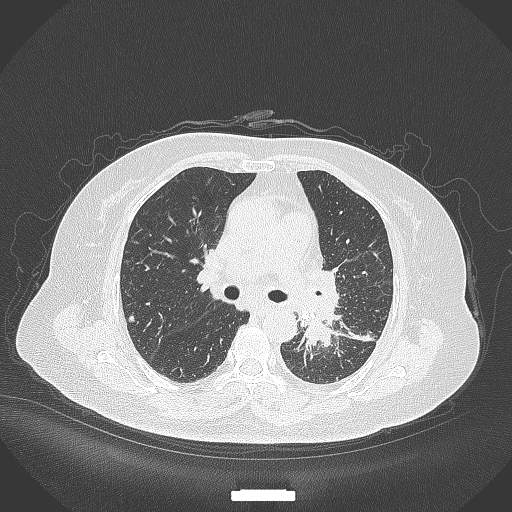
Chest CT, one axial slice; slice 210 of 322 in the series (ordered by position); lung window (W 1500 / L -600 HU); 1 mm slice thickness; 512 × 512 image matrix. Female patient, age 69 years. Case-level facts recorded for this patient, not image findings: clinical TNM (as recorded): T2b N3 M1.
Outlined on this slice (bounding box drawn by a radiologist):
- lung tumour (recorded histology: adenocarcinoma): bounding box [x1, y1, x2, y2] px = [292, 313, 334, 367]